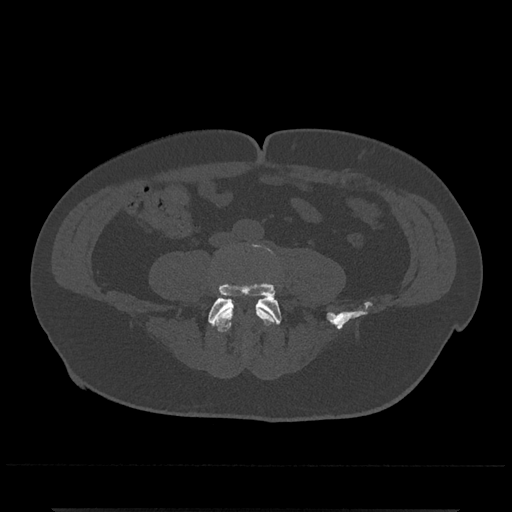
CT including the spine, one axial slice; 120 kVp; bone window (W 1800 / L 400 HU); 0.5 mm slice thickness; 512 × 512 image matrix, field of view 393 × 393 mm. Patient: male, 67 years. Case-level facts recorded for this patient, not image findings: primary cancer: prostate.
Structures marked on this image (semi-automatic segmentation, software-assisted and operator-edited):
- L4 vertebra: bounding box <212,301,278,332> (left, top, right, bottom; pixels)
- L5 vertebra: <208,244,282,327>